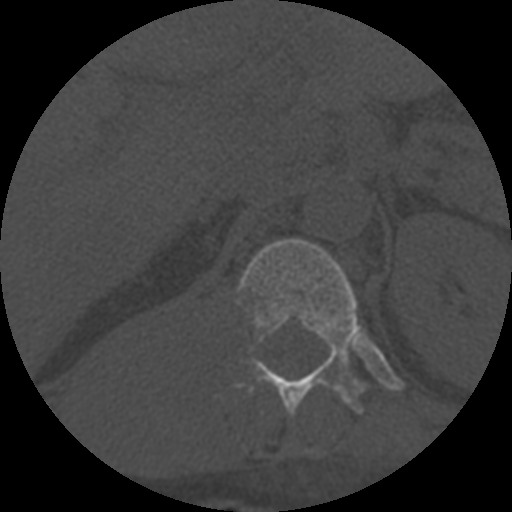
CT including the spine, one axial slice; position 314 of 708 along the scan axis; 120 kVp; one of 3 acquisitions stored at this slice position; bone window (W 1800 / L 400 HU); 512 × 512 image matrix, field of view 160 × 160 mm. Patient age 55 years. From the clinical record (not read from this slice): primary cancer: colon; vertebrae with lytic lesions (as recorded): T12, L1, L5.
Annotated regions visible in this slice (semi-automatically segmented with operator editing):
- T12 vertebra: box from (x=237, y=238) to (x=365, y=414) px